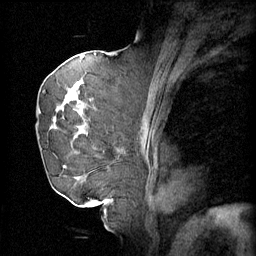
Breast MRI (dynamic contrast-enhanced), one sagittal slice. Slice 31 of 60 in the series (ordered by position). 4 images stored at this slice position (order not interpretable as contrast timing). 1.5 T. TE 4.2 ms, TR 11 ms. 2 mm slice thickness. 256 × 256 image matrix, field of view 220 × 220 mm. Female patient, age 72 years.
Outlined on this slice (semi-automatically segmented with operator editing):
- analysis volume of interest (the breast-tissue region the enhancement analysis was run in; not a lesion): bounding box <43,68,101,163> (left, top, right, bottom; pixels)
- tumour enhancement mask (voxels above the 70 % enhancement threshold inside the analysis volume of interest): <44,76,96,151>